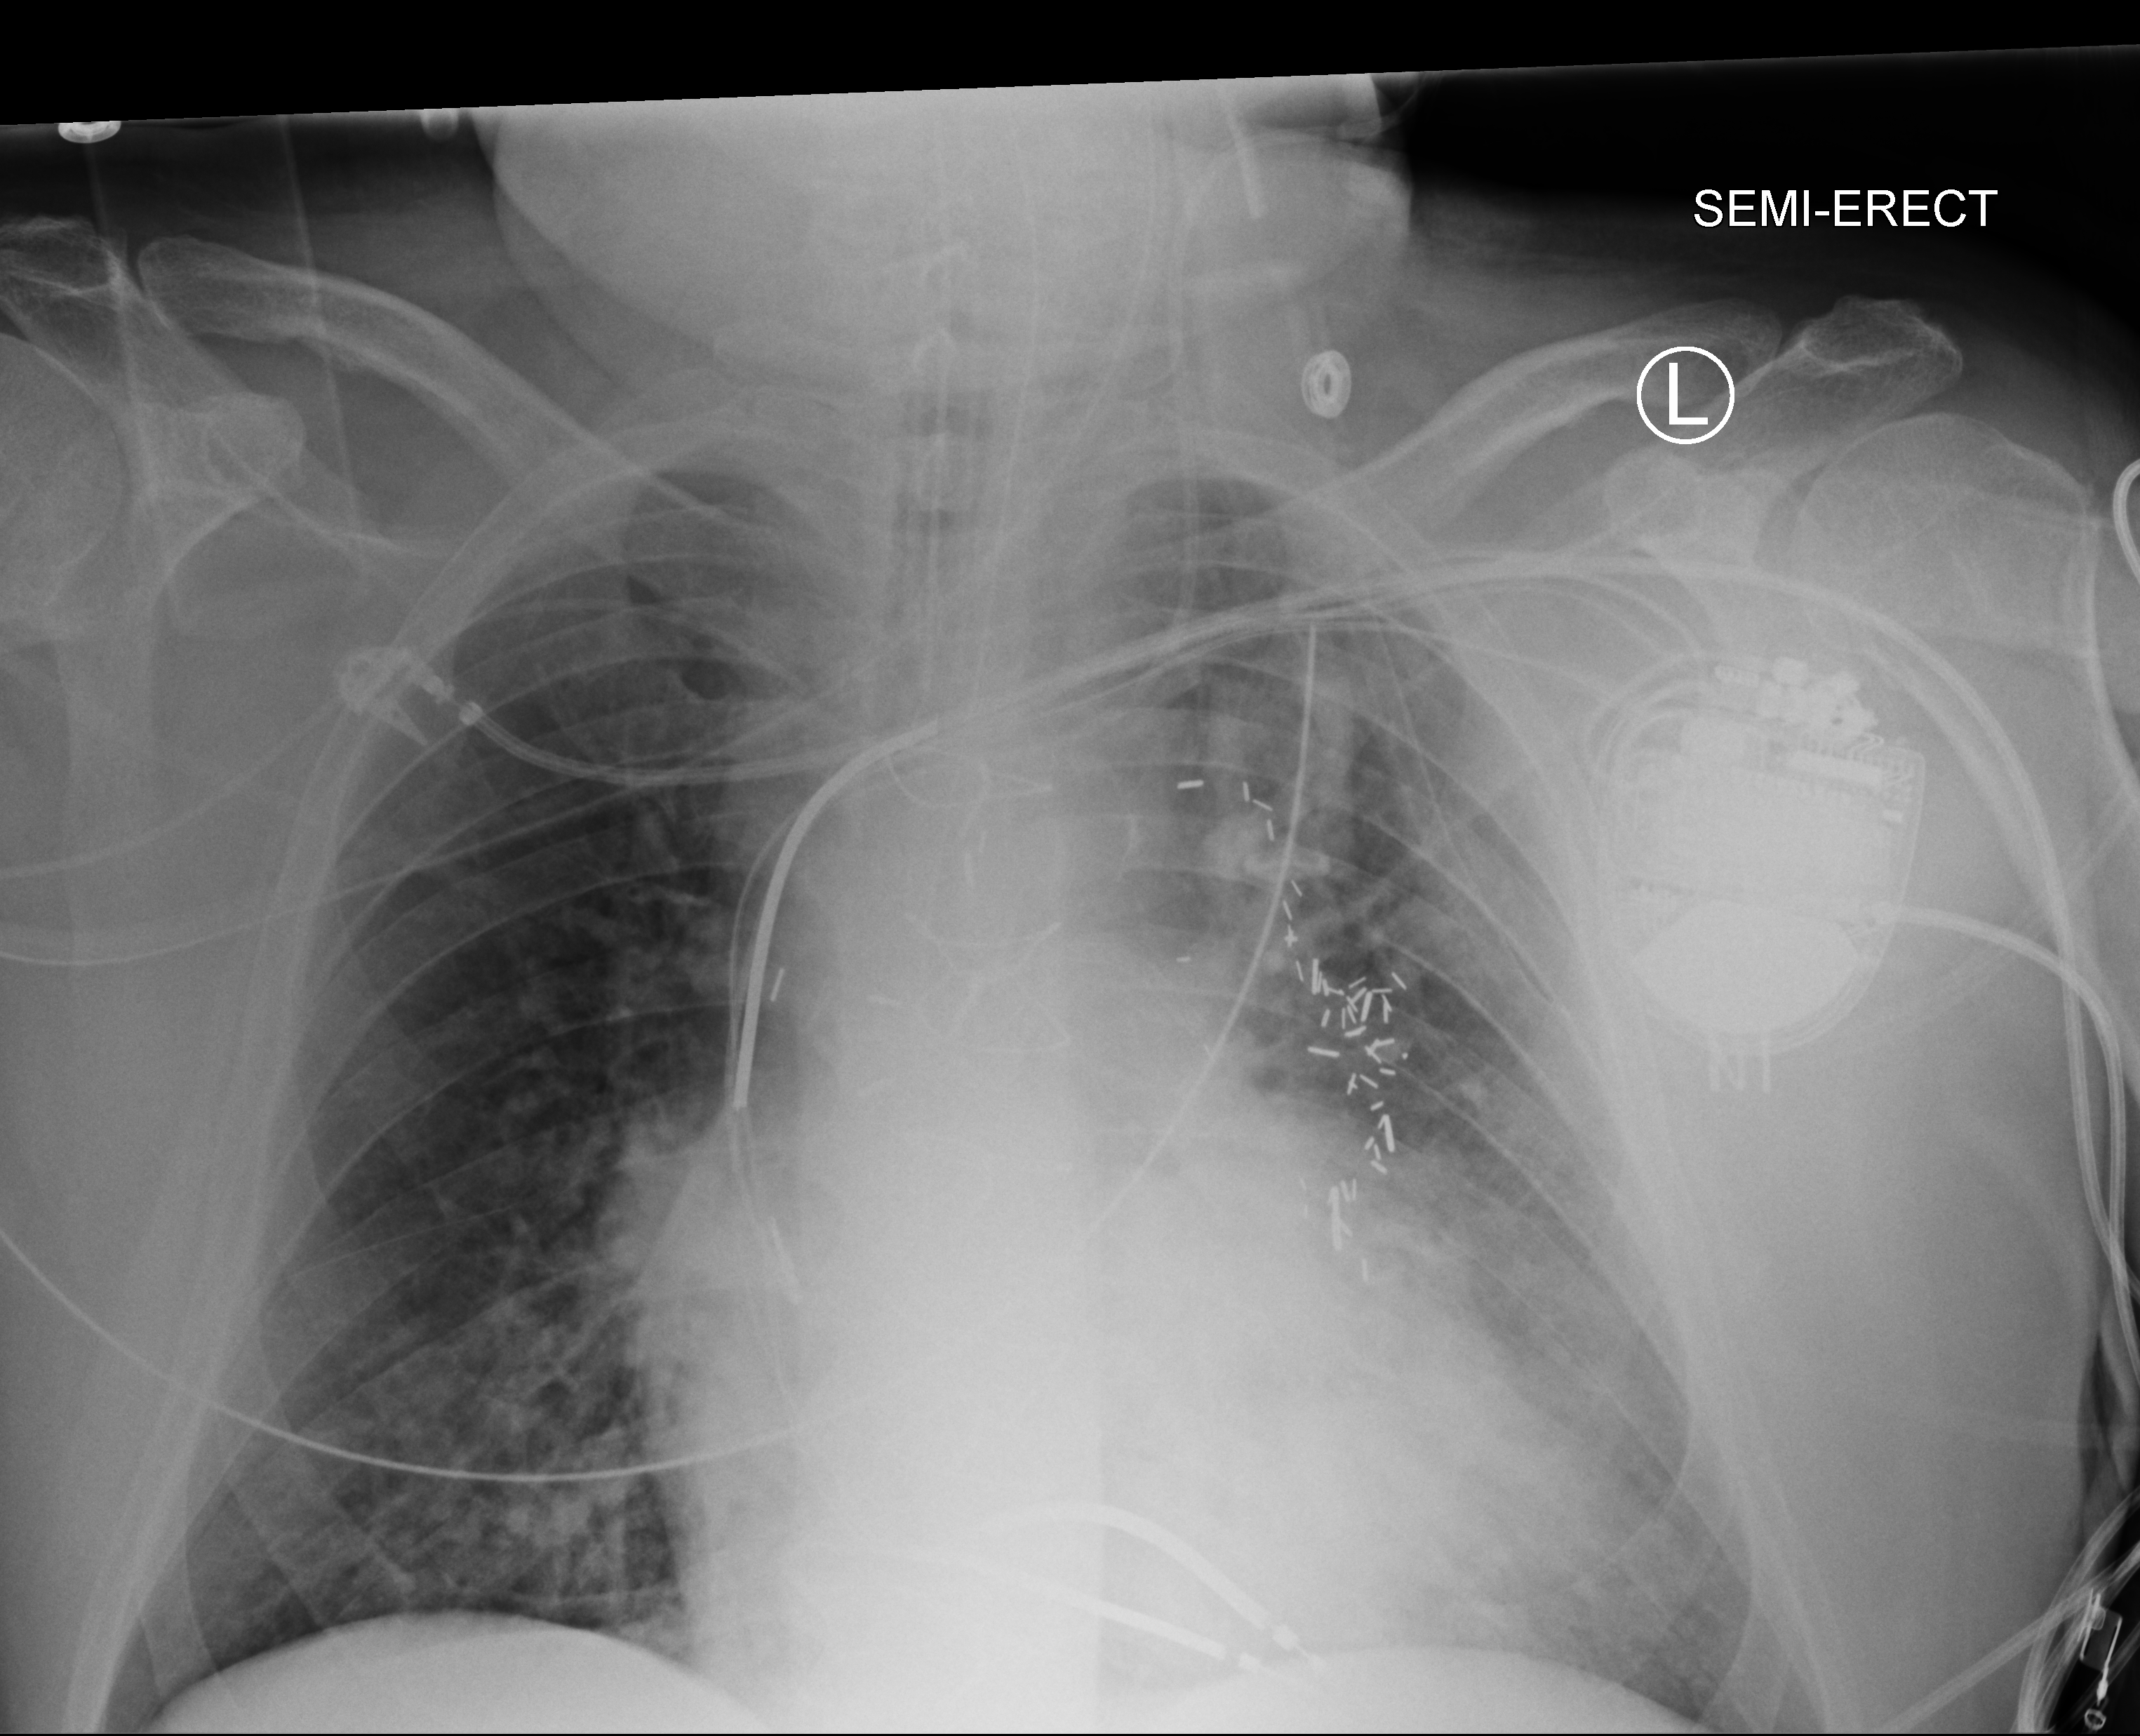
Bedside chest radiograph (computed radiography); anteroposterior (AP) projection. Patient hospitalised with COVID-19; male, aged 60–74 years.
From the hospital-stay record, not from the radiograph (when in the stay this image was taken is not recorded): COPD (admission record): no; mechanically ventilated during this hospital stay: yes.